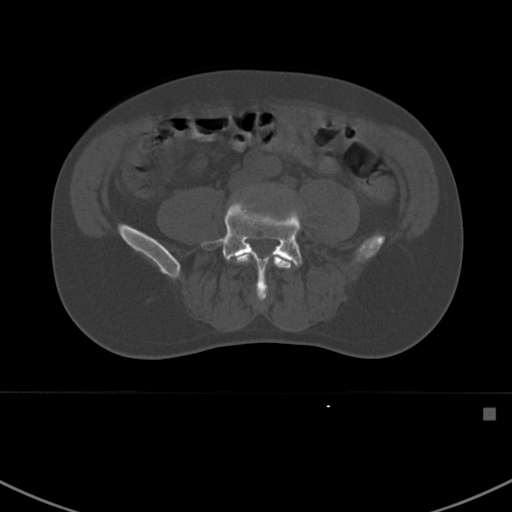
CT including the spine, one axial slice. Slice 227 of 412 in the series (ordered by position). Reconstruction kernel Br40s. 120 kVp. Bone window (W 1800 / L 400 HU). 1.5 mm slice thickness. 512 × 512 image matrix. Patient: male, 59 years. From the clinical record (not read from this slice): primary cancer: prostate.
Structures marked on this image (semi-automatic segmentation, software-assisted and operator-edited):
- L4 vertebra: bounding box (x1, y1, x2, y2) in pixels: (235, 252, 292, 299)
- L5 vertebra: (201, 198, 302, 300)